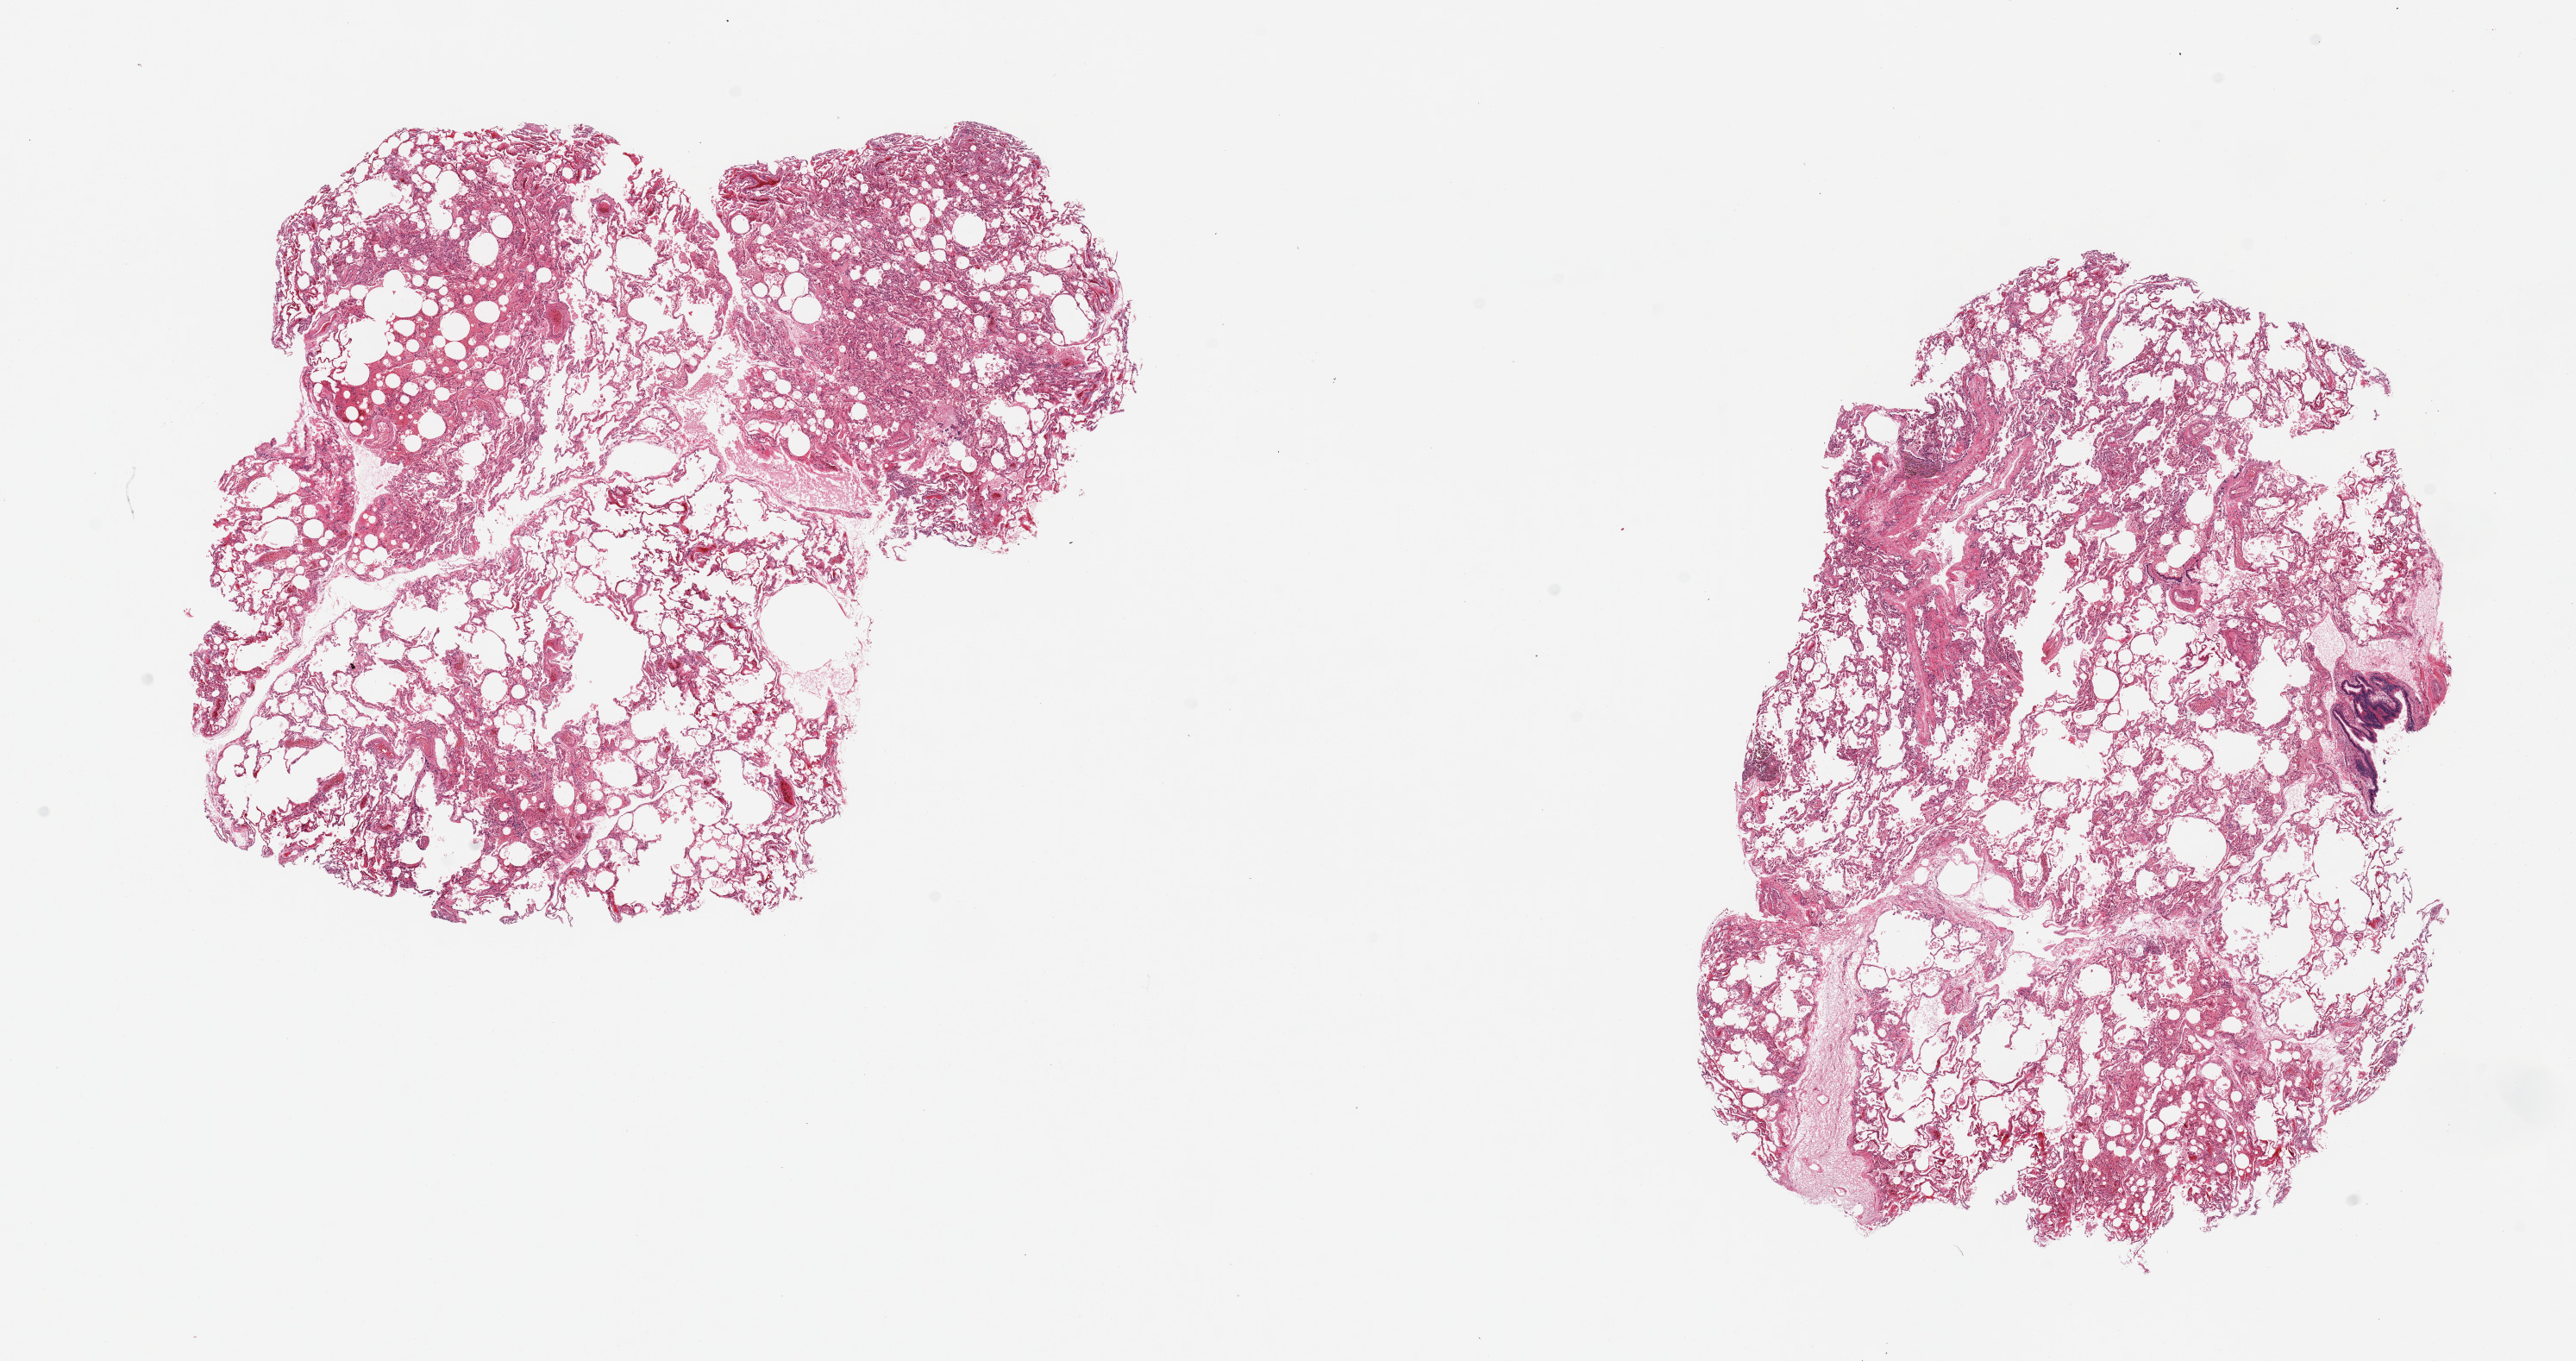
Whole-slide image, hematoxylin and eosin (H&E) stain, brightfield — whole scanned area (about 23.6 x 12.5 mm) shown as a low-resolution overview. PAXgene-fixed paraffin-embedded (PFPE) section. Target tissue: lung. Tissue donor sample. Donor: male.
Pathologist's review note for this sample: 2 pieces; some congestion/hemorrhage and emphysematous change.